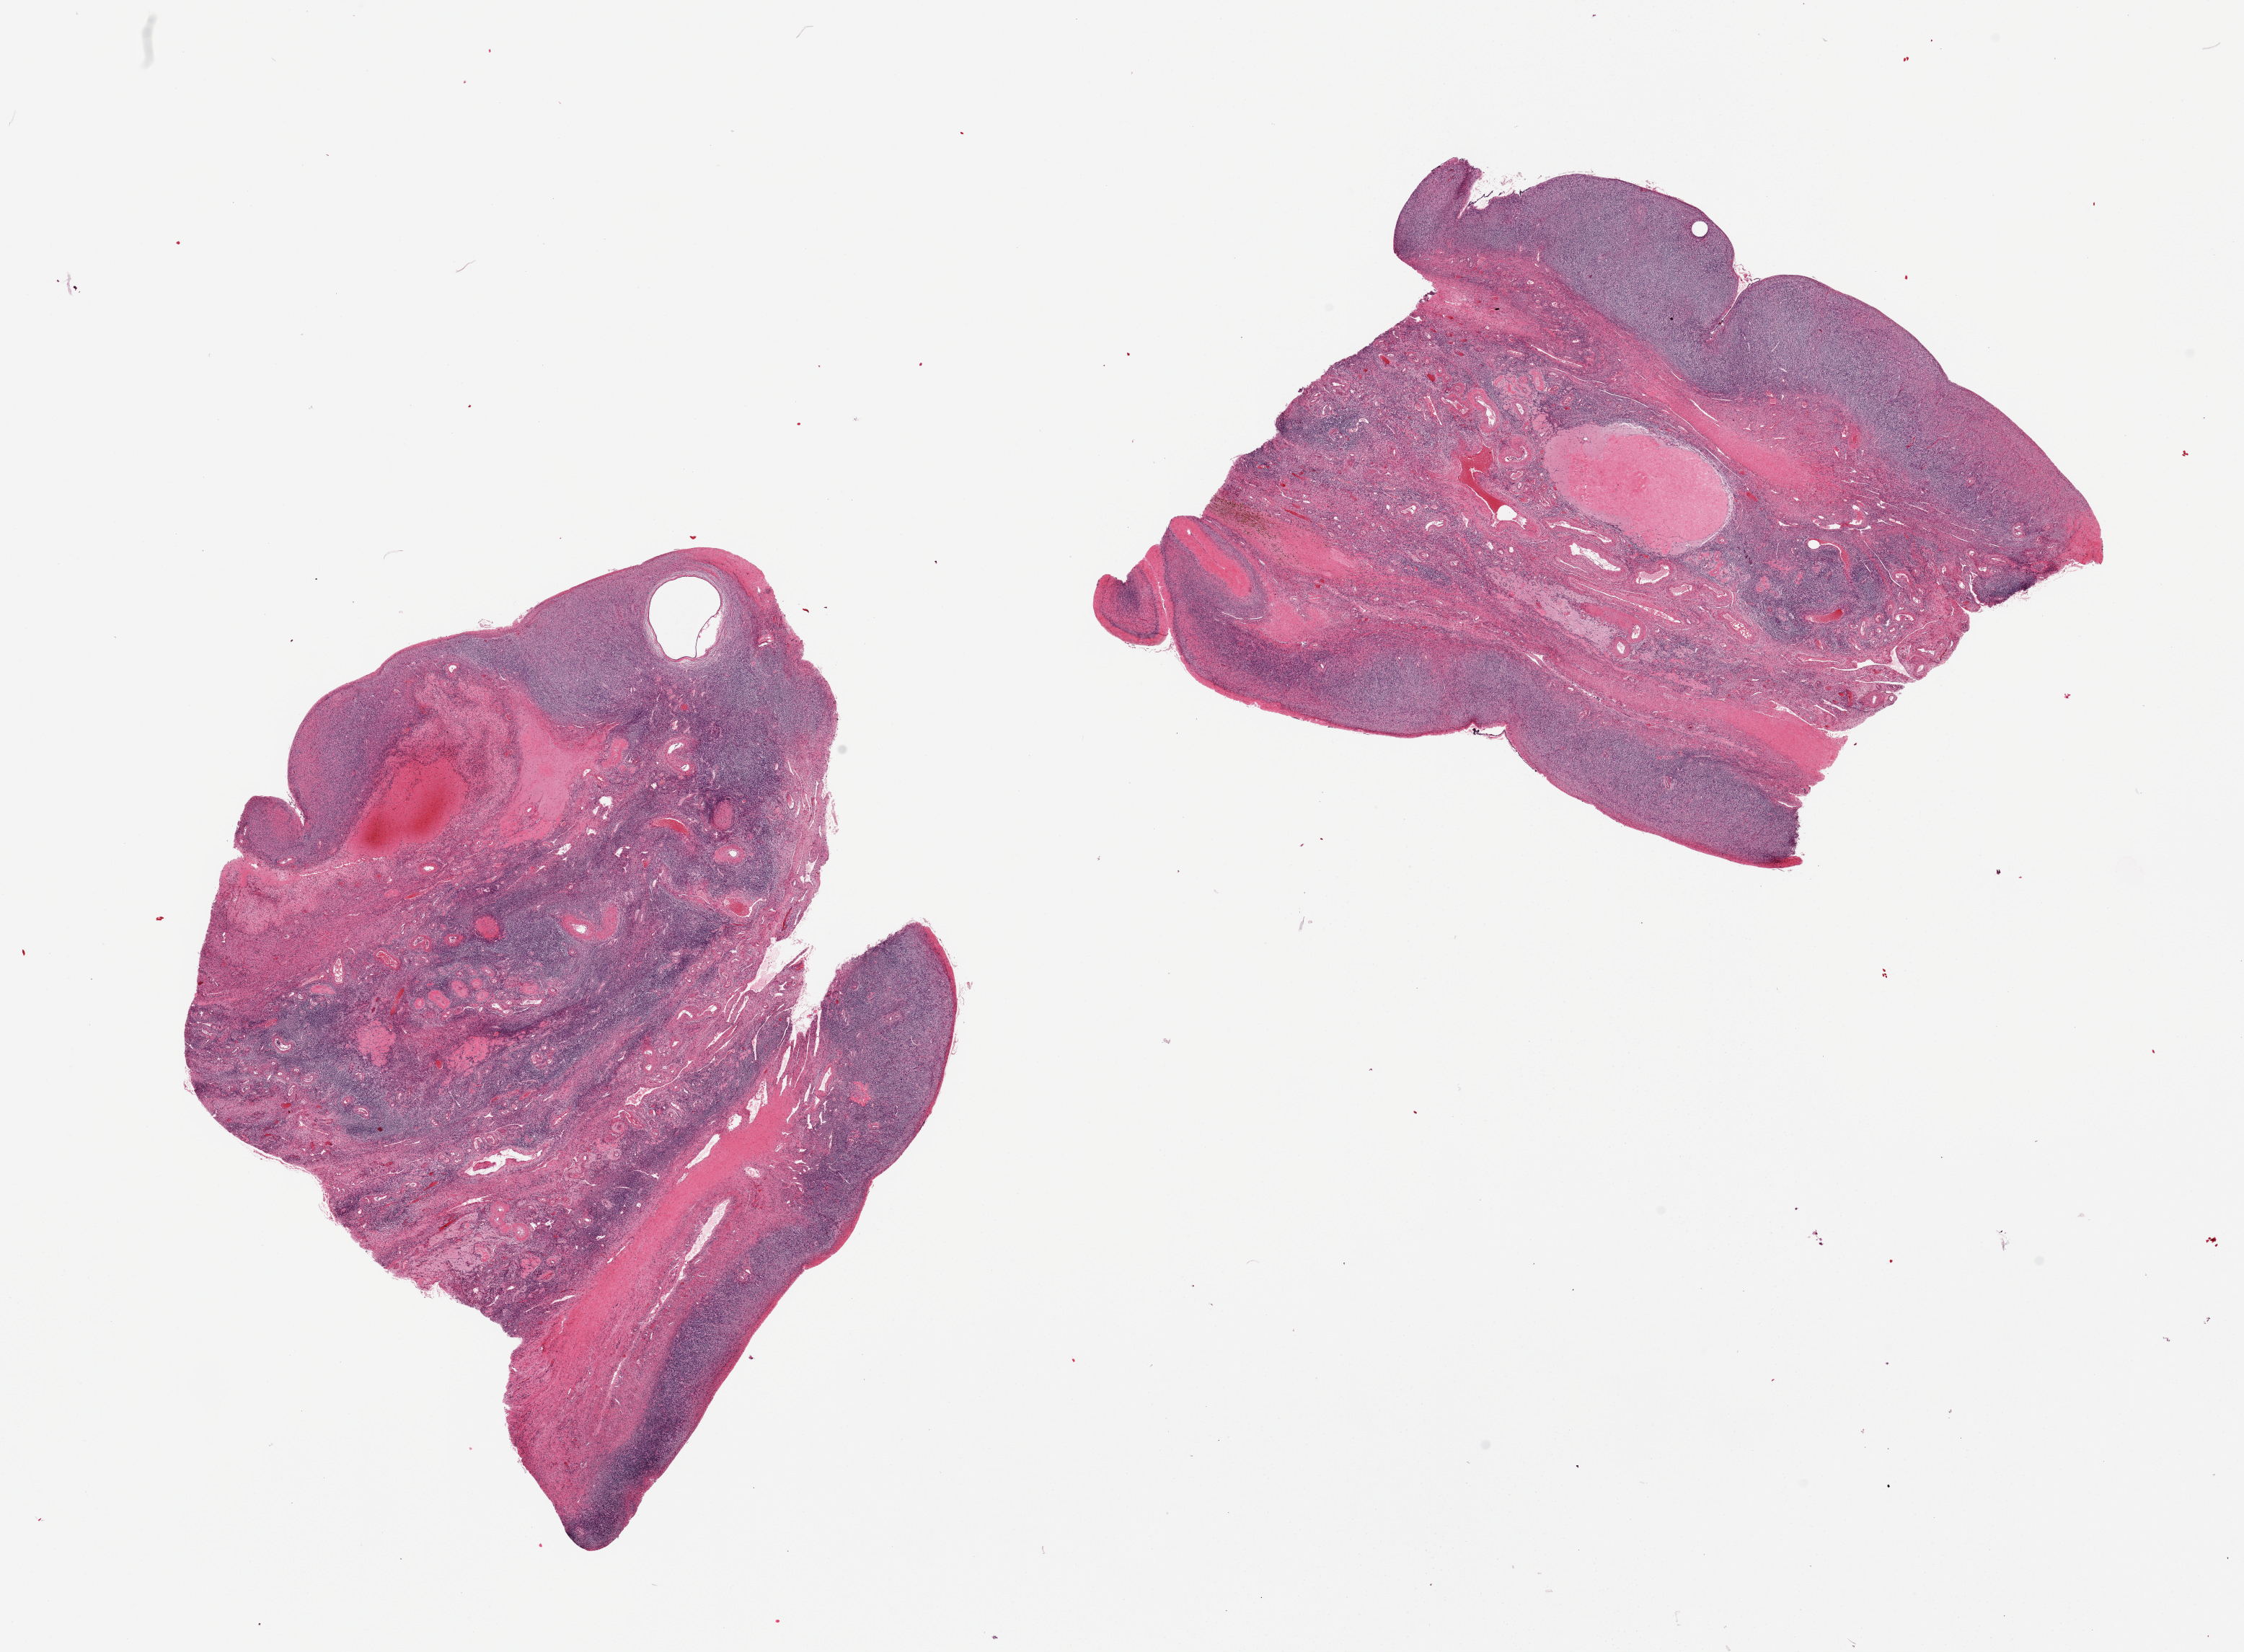
Digitized hematoxylin and eosin (H&E)-stained section, brightfield, low-resolution overview of the scanned area, about 24.6 x 18.1 mm; PAXgene-fixed, paraffin-embedded tissue; section of ovary (target tissue); donor tissue sample. Donor sex: female.
Pathologist's review note for this sample: 2 pieces, typical post menopopausal appearance, unremarkable.